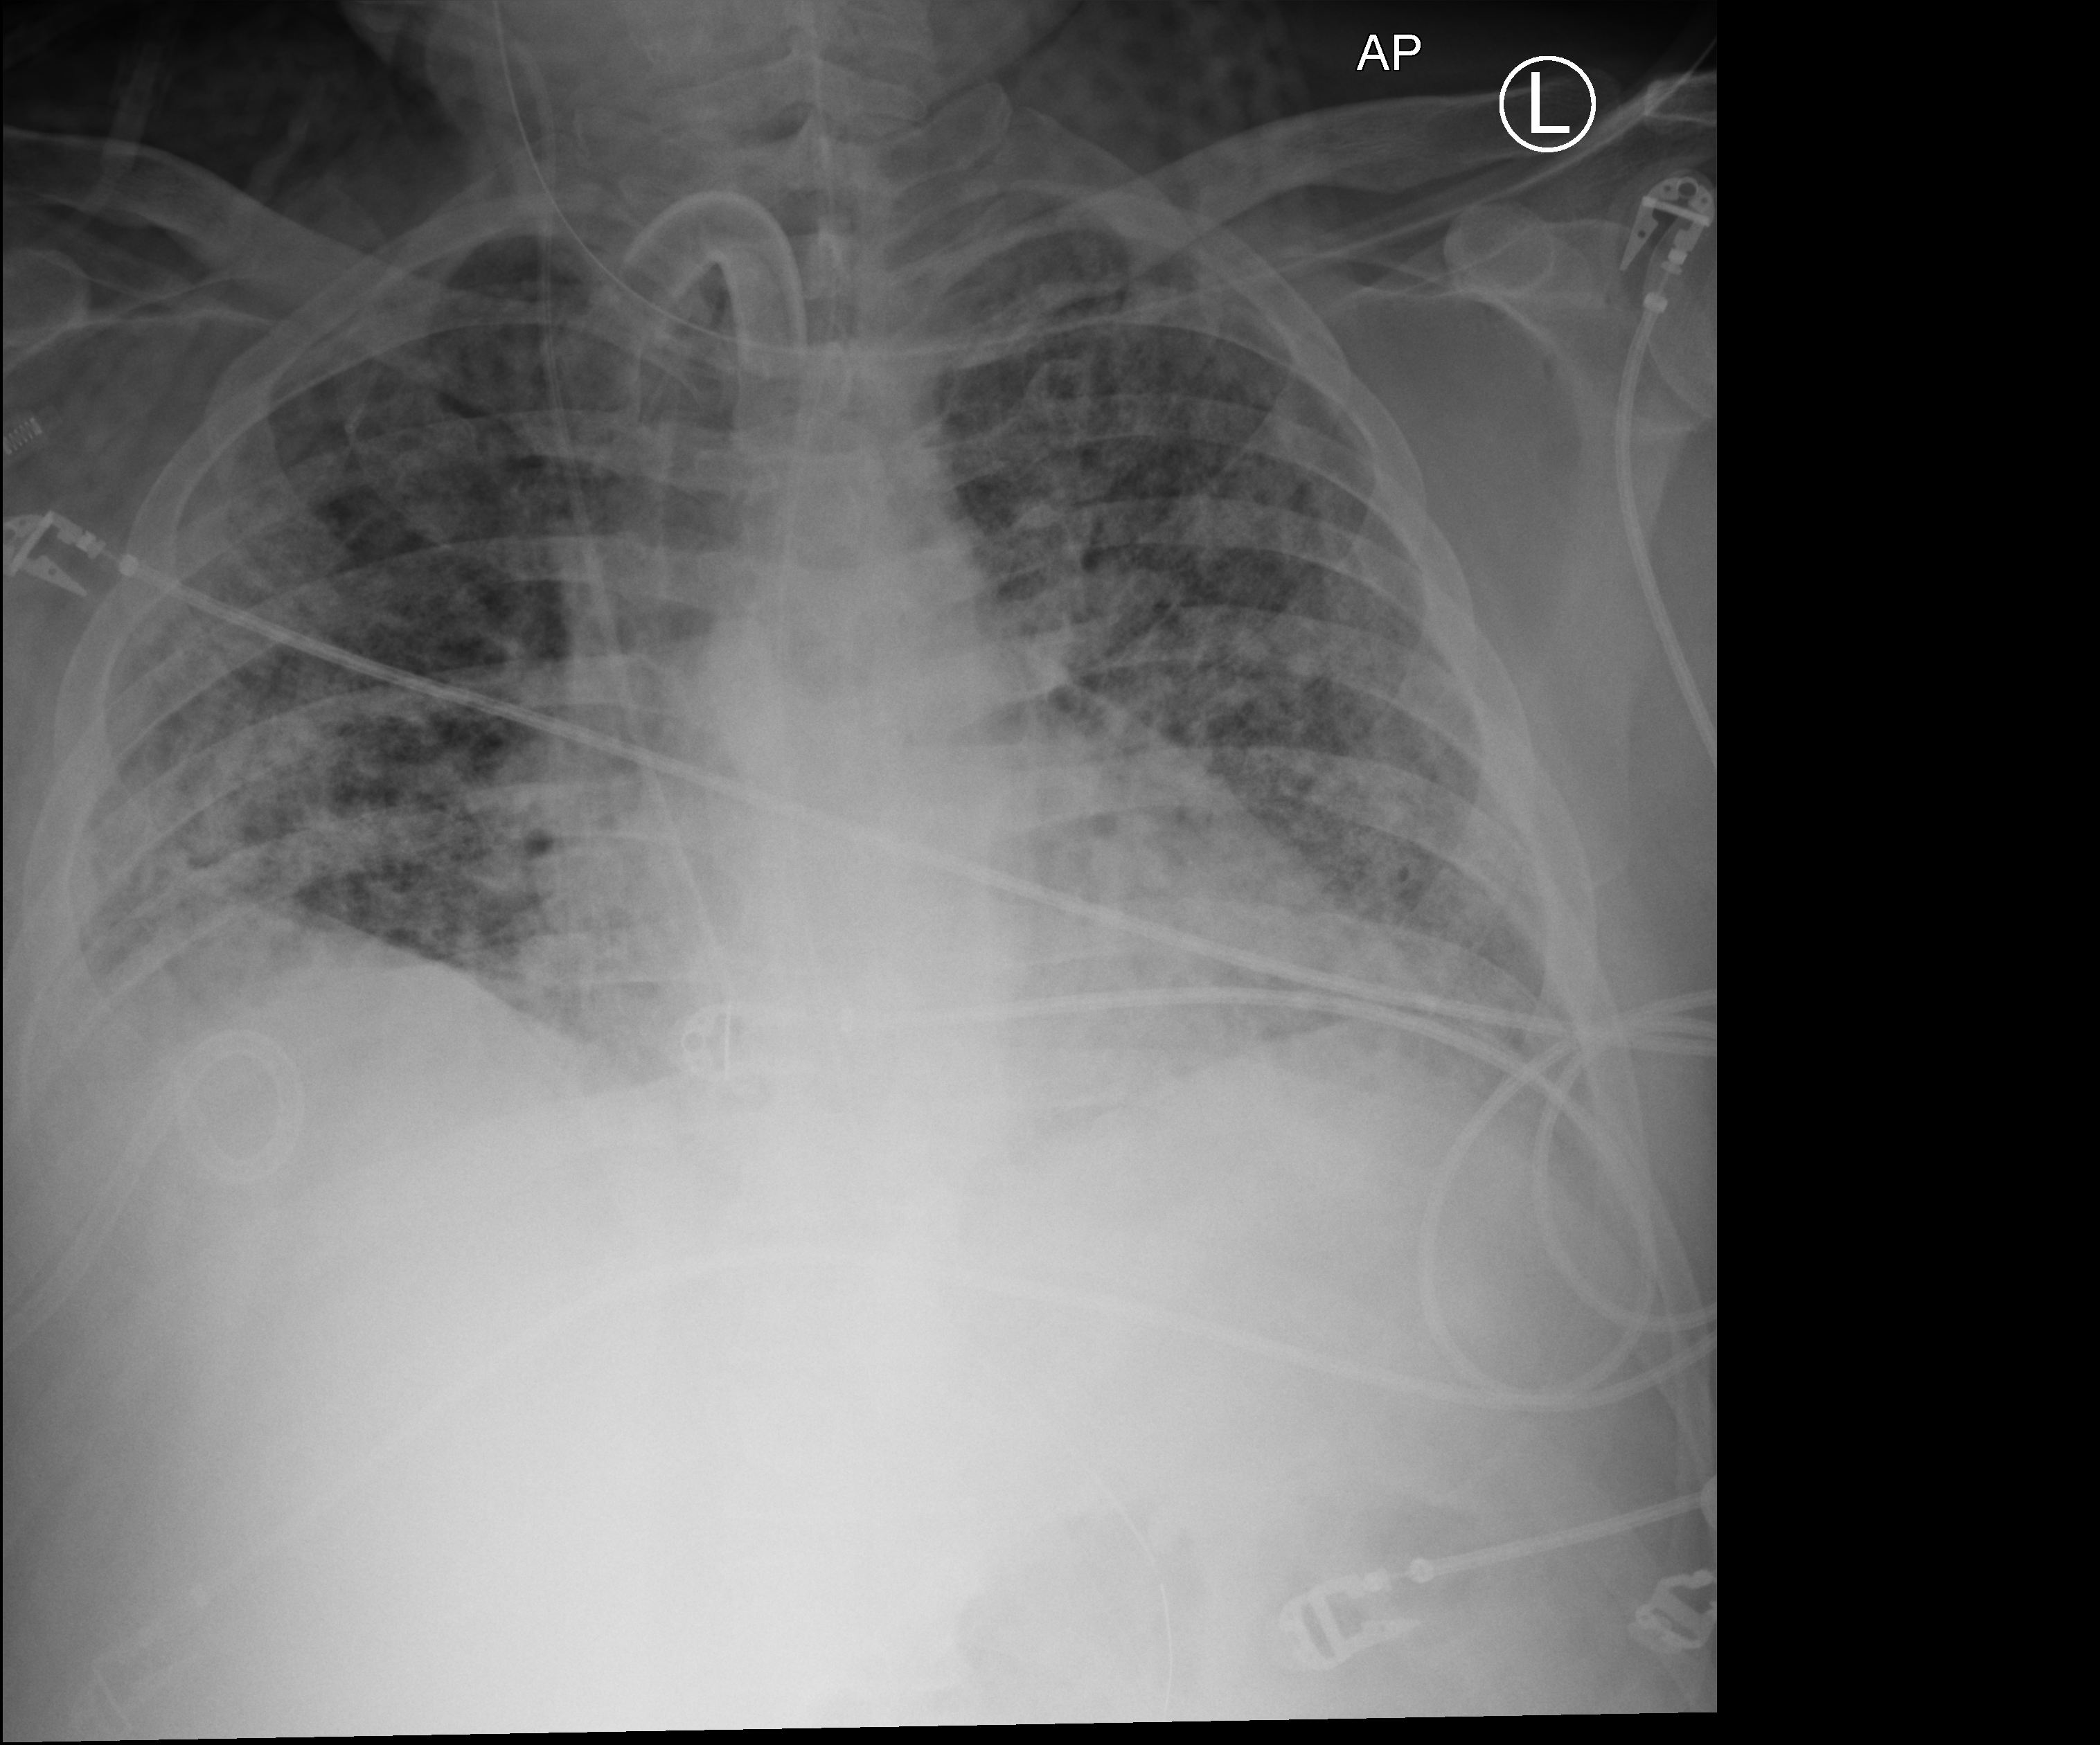
Bedside chest radiograph (computed radiography), anteroposterior (AP) projection. Male patient hospitalised with COVID-19, age 18–59 years.
Hospital-stay facts (about this admission, not read from this image; timing relative to this image not recorded): admitted to intensive care during this hospital stay: yes; mechanically ventilated during this hospital stay: yes.